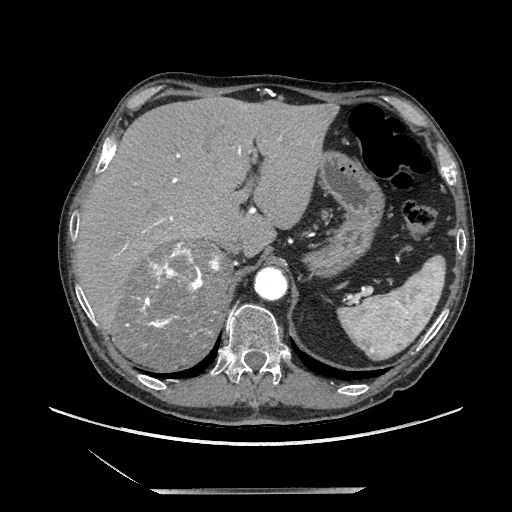
Contrast-enhanced abdominal CT, one axial slice. Slice 157 of 243 in the series (ordered by position). Soft-tissue window (W 400 / L 40 HU). 512 × 512 image matrix, field of view 420 × 420 mm. Male patient. Case-level facts recorded for this patient, not image findings: diagnosis: adrenocortical carcinoma; tumour side: right adrenal; tumour size at pathology: 16 cm; Ki-67 index: 17 %; stage (as recorded): 3.
Annotated regions visible in this slice (semi-automatic segmentation, software-assisted and operator-edited):
- mass: box from (x=116, y=243) to (x=228, y=368) px